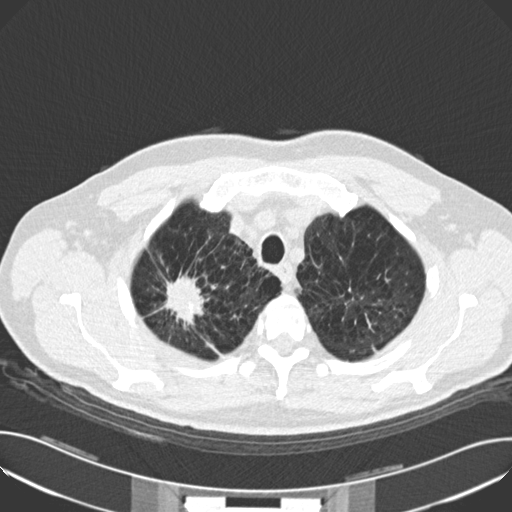
Low-dose screening chest CT, one axial slice. Slice 137 of 159 in the series (ordered by position). Reconstruction kernel B30f. 120 kVp. Lung window (W 1500 / L -600 HU). 512 × 512 image matrix, field of view 380 × 380 mm.
Outlined on this slice (manually delineated by an expert):
- lesion 1 (tumor, upper lobe of right lung): bounding box (x1, y1, x2, y2) in pixels: (165, 275, 203, 321)